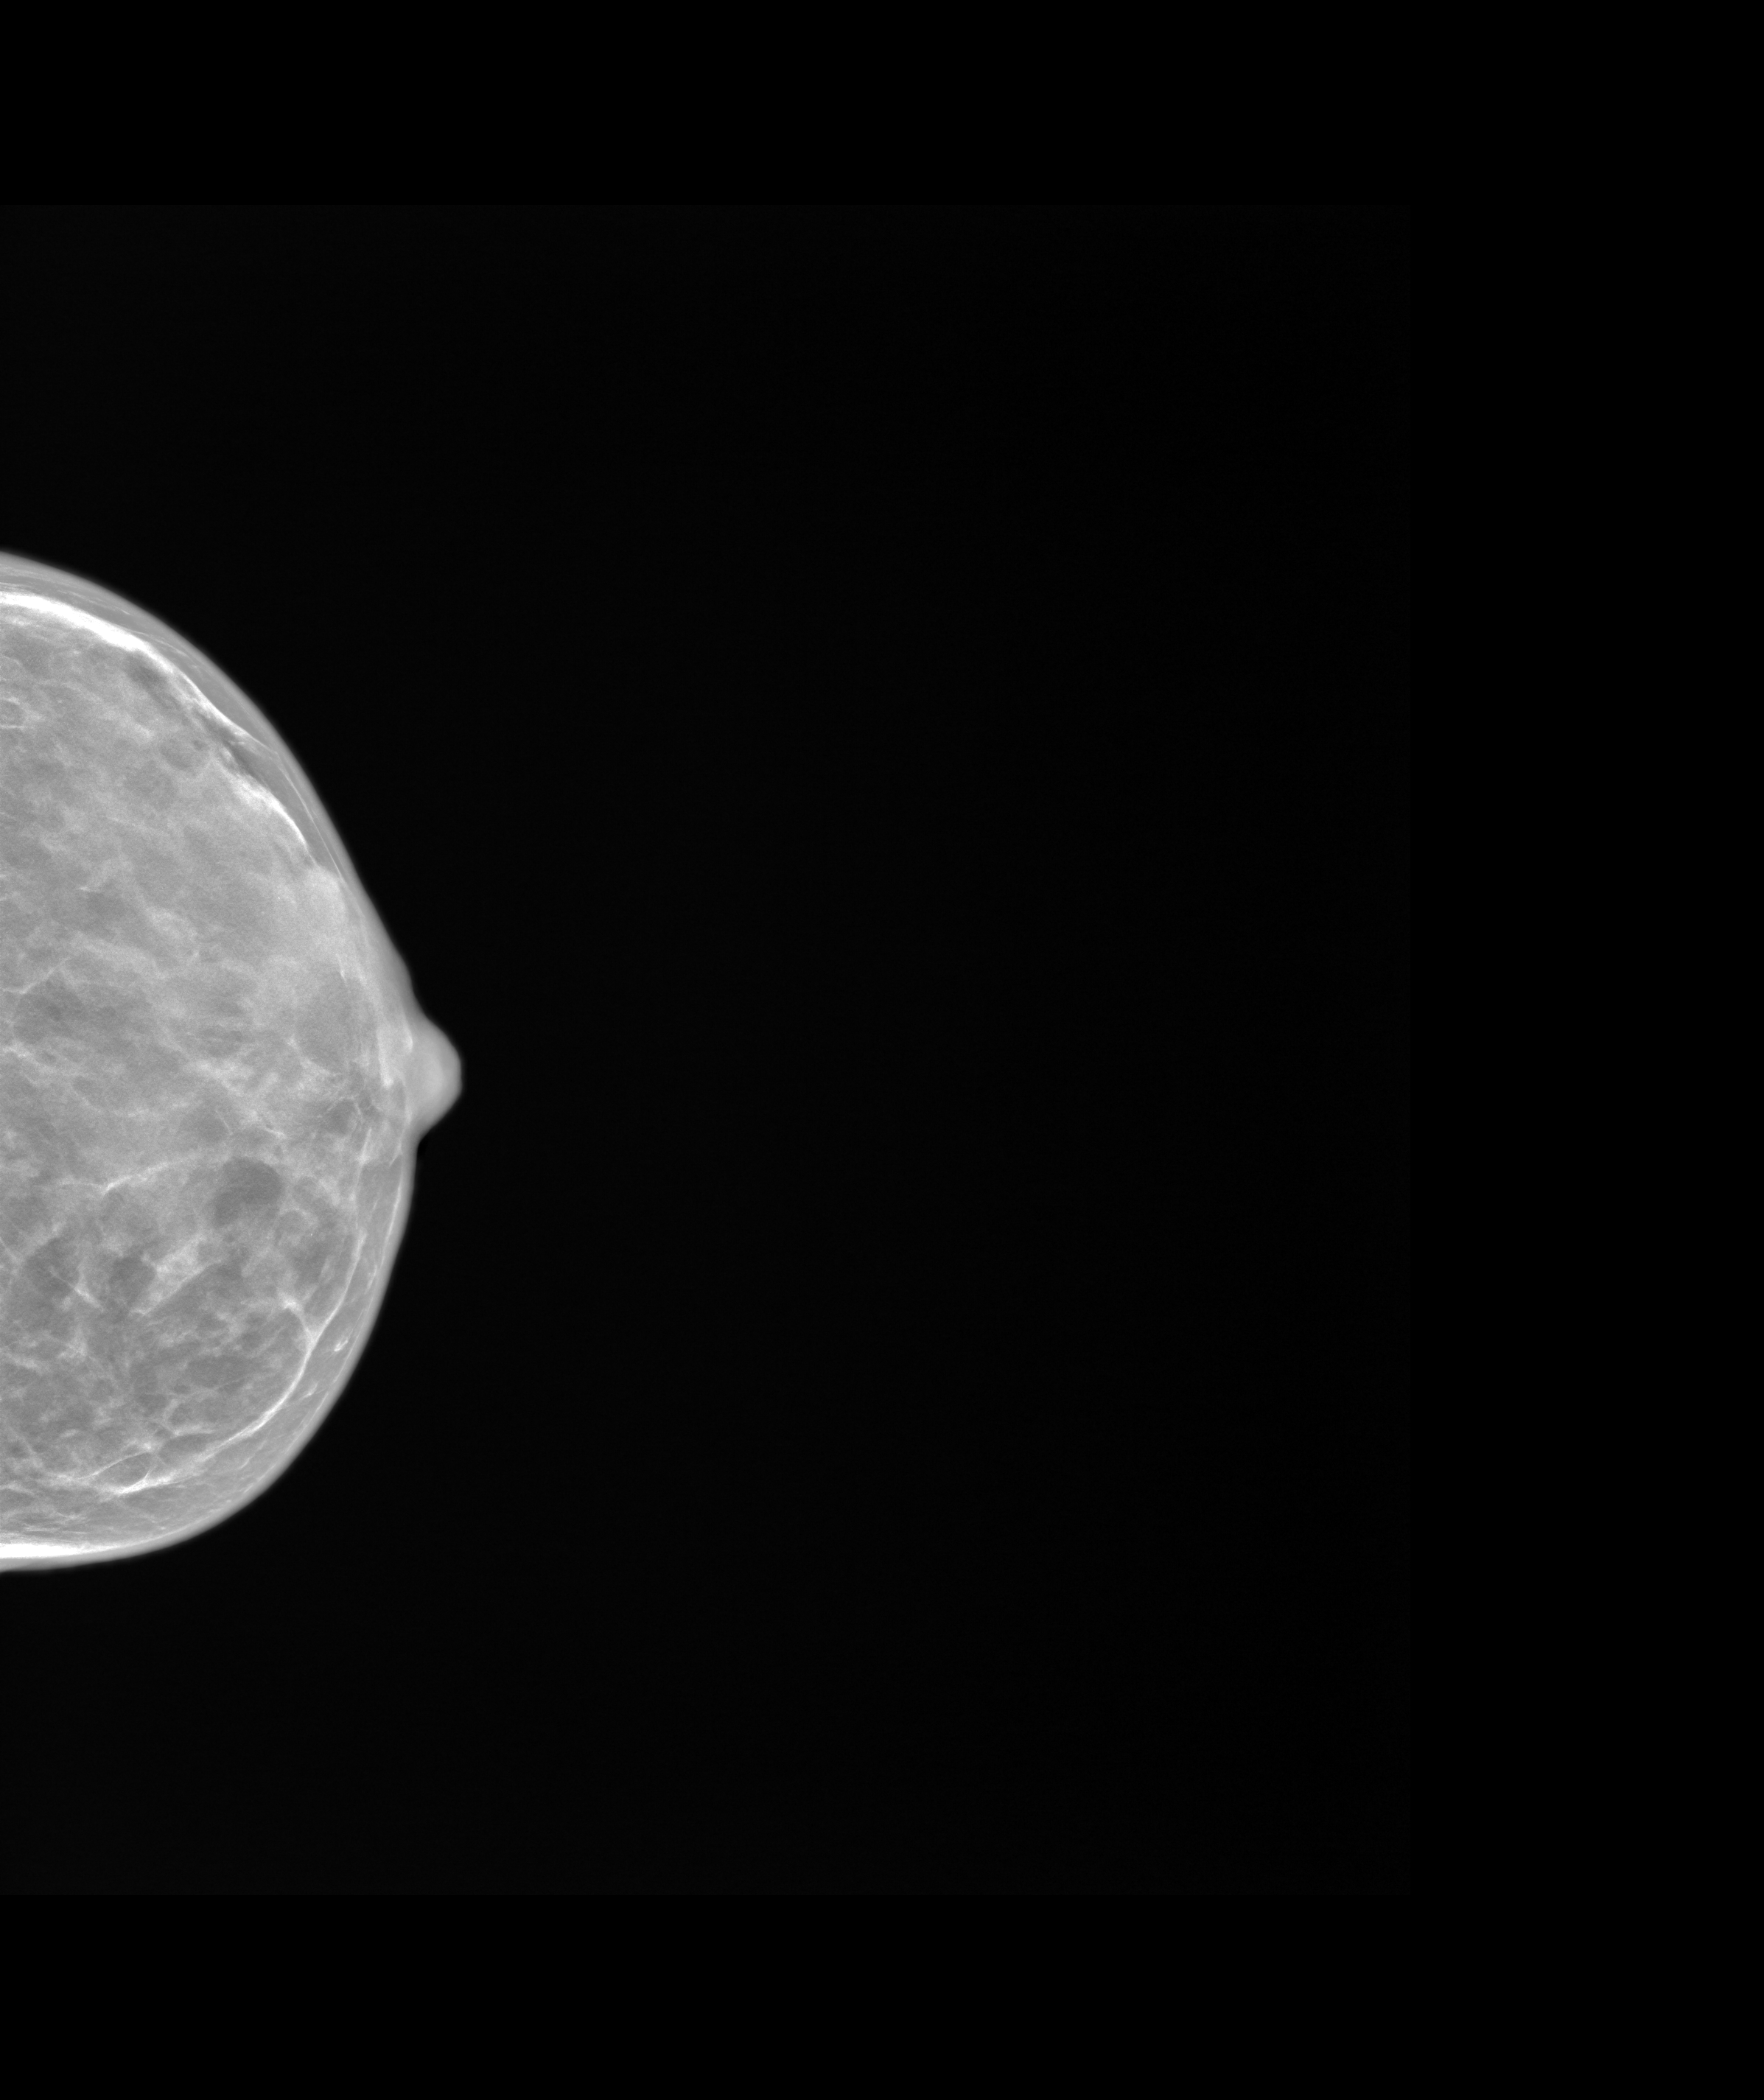
Synthesized 2-D mammogram reconstructed from digital breast tomosynthesis; left breast; cranio-caudal projection; screening examination. Patient aged 54 years (female).
- breast density at the screening exam (both breasts): extremely dense (BI-RADS density category d)
- final BI-RADS assessment for this screening round (tomosynthesis exam, both breasts): category 1
- recall: no recall after this screen